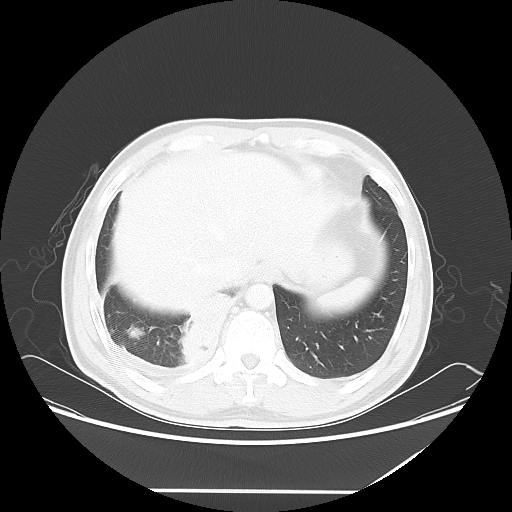
Chest CT, one axial slice; position 14 of 60 along the scan axis; reconstruction kernel LUNG; lung window (W 1500 / L -600 HU); 5 mm slice thickness; 512 × 512 image matrix. Male patient, age 48 years. Case-level facts recorded for this patient, not image findings: clinical TNM (as recorded): T3 N3 M1a.
Annotated regions visible in this slice (rectangle marked by the reading radiologist):
- lung tumour (recorded histology: squamous cell carcinoma): bounding box <177,290,235,371> (left, top, right, bottom; pixels)